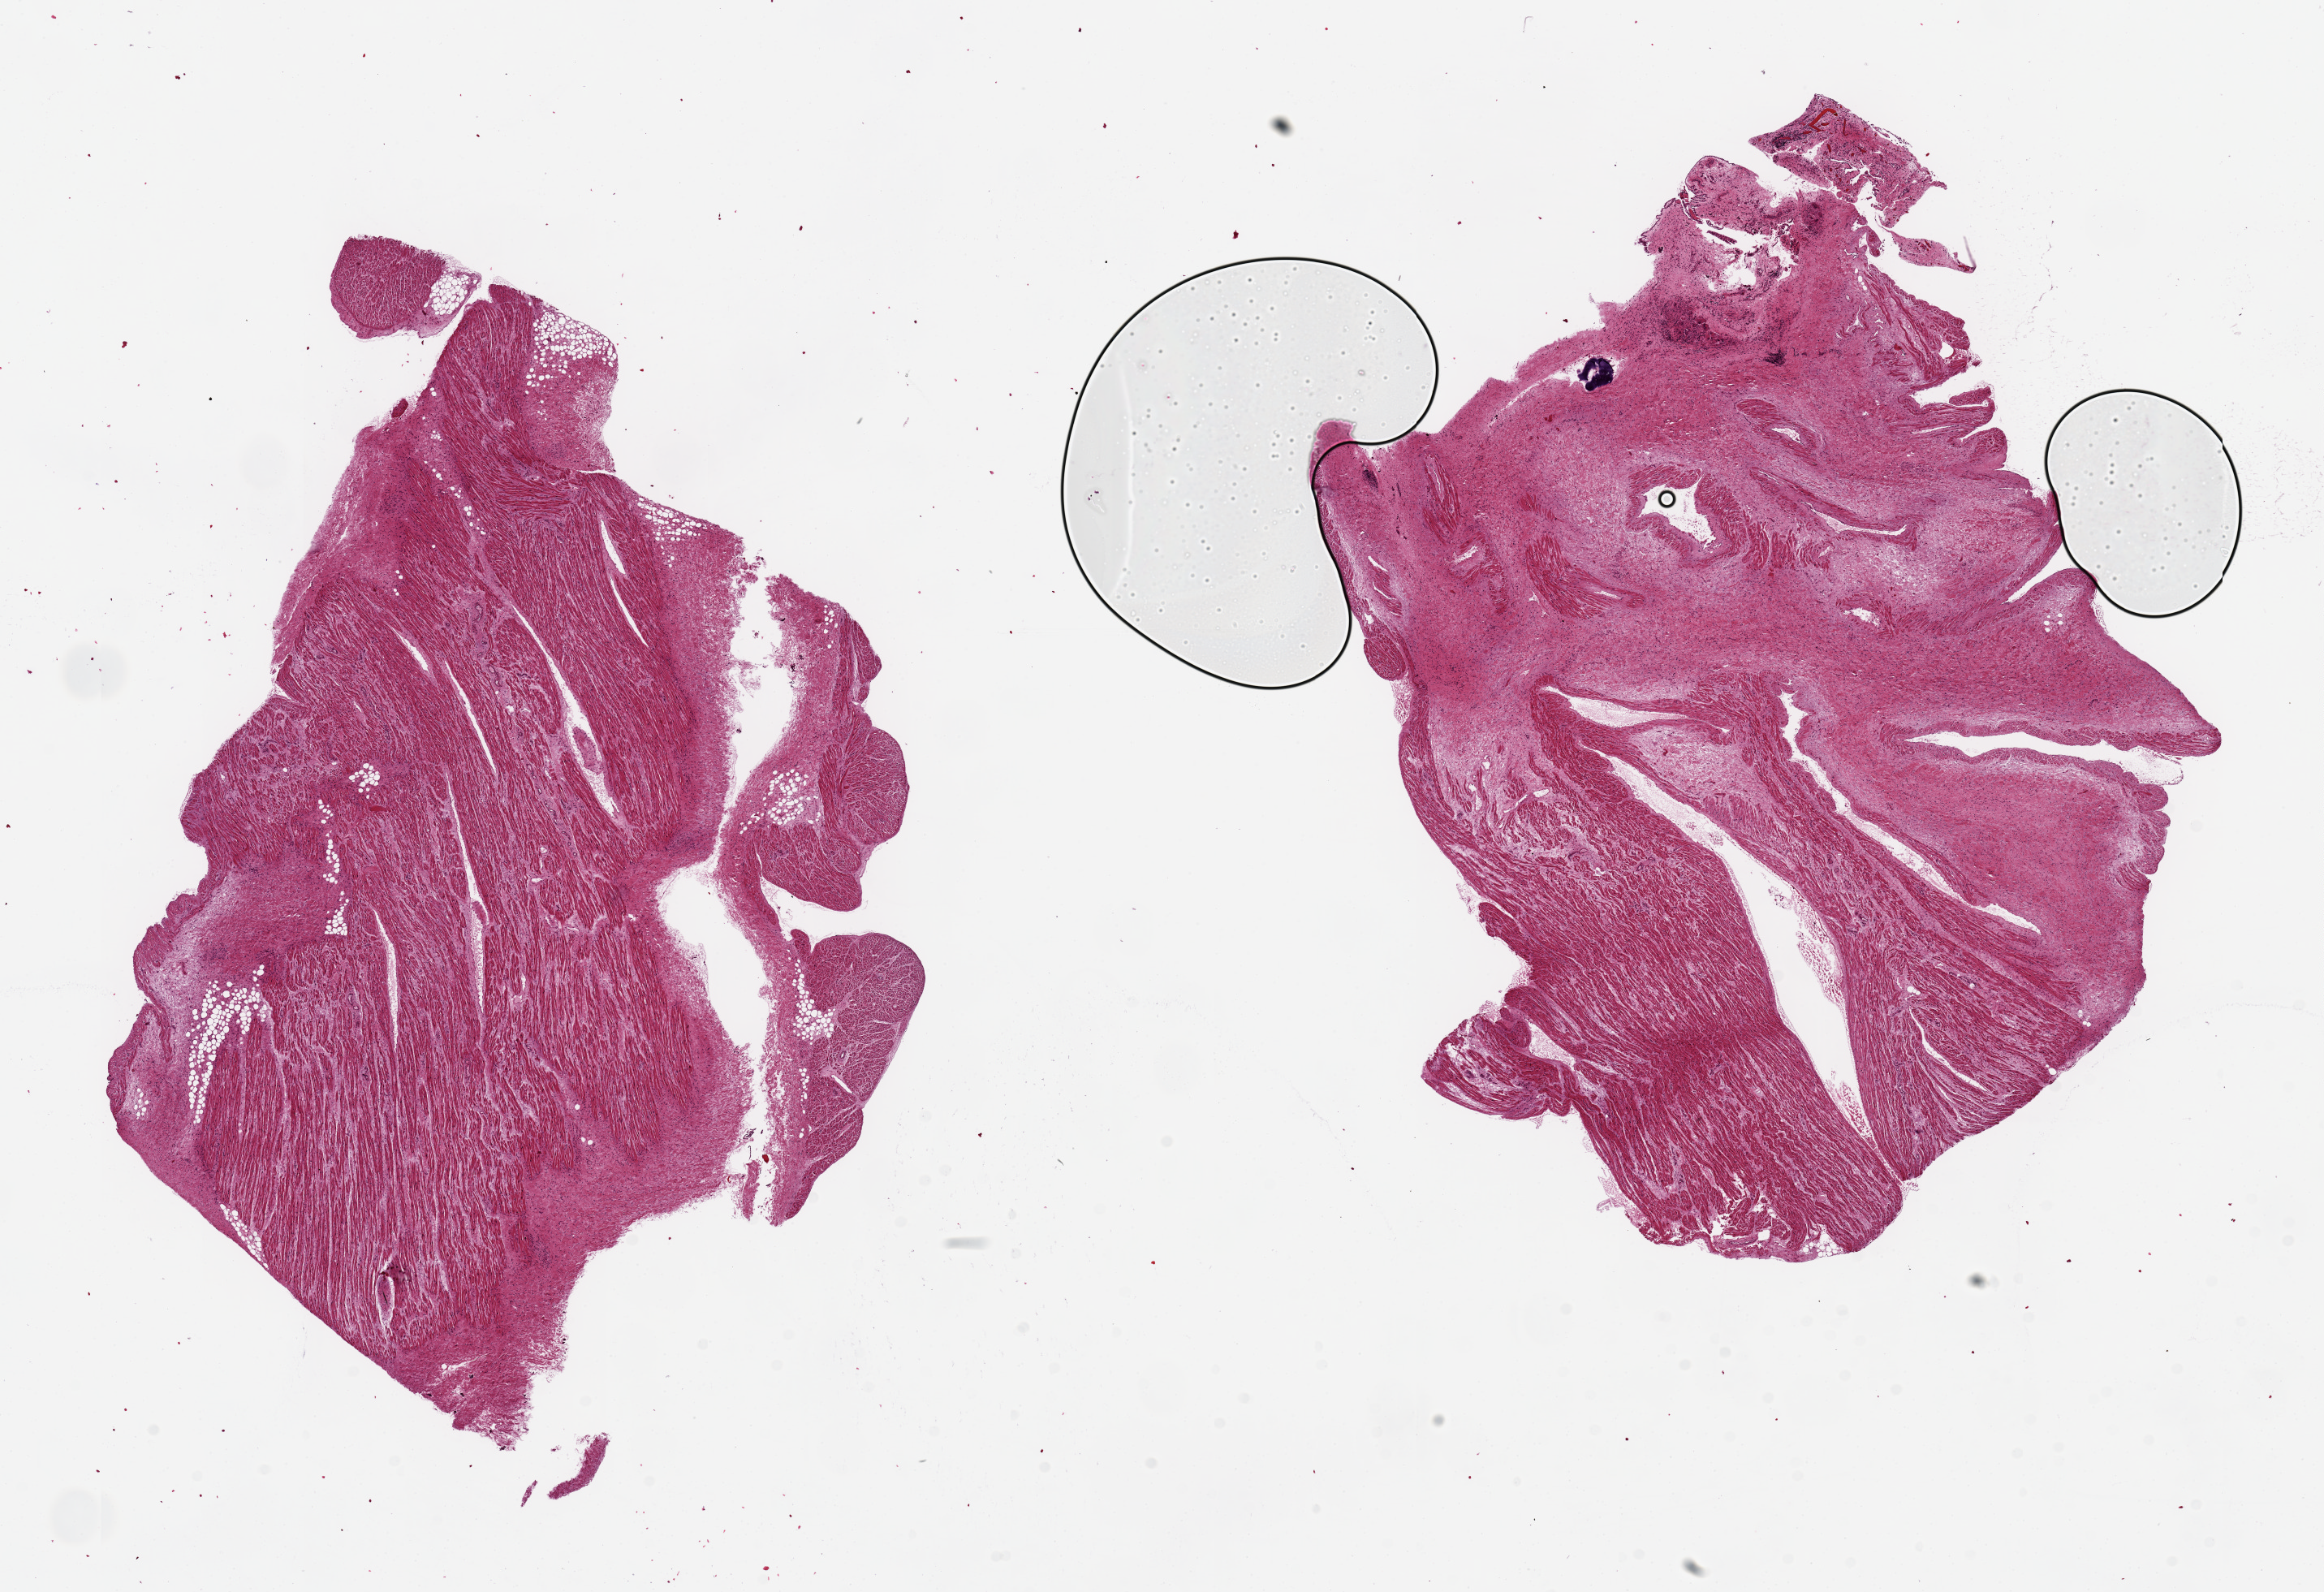
Whole-slide image, H&E stain, whole scanned area (about 22.6 x 15.5 mm) shown as a low-resolution overview; PAXgene-fixed paraffin-embedded (PFPE) section; section of auricular appendage (target tissue); donor tissue sample.
Reviewer comment on this tissue sample: 2 pieces, 9x8.5 & 10x9mm; up to 50% interstitial fibrous tissue.